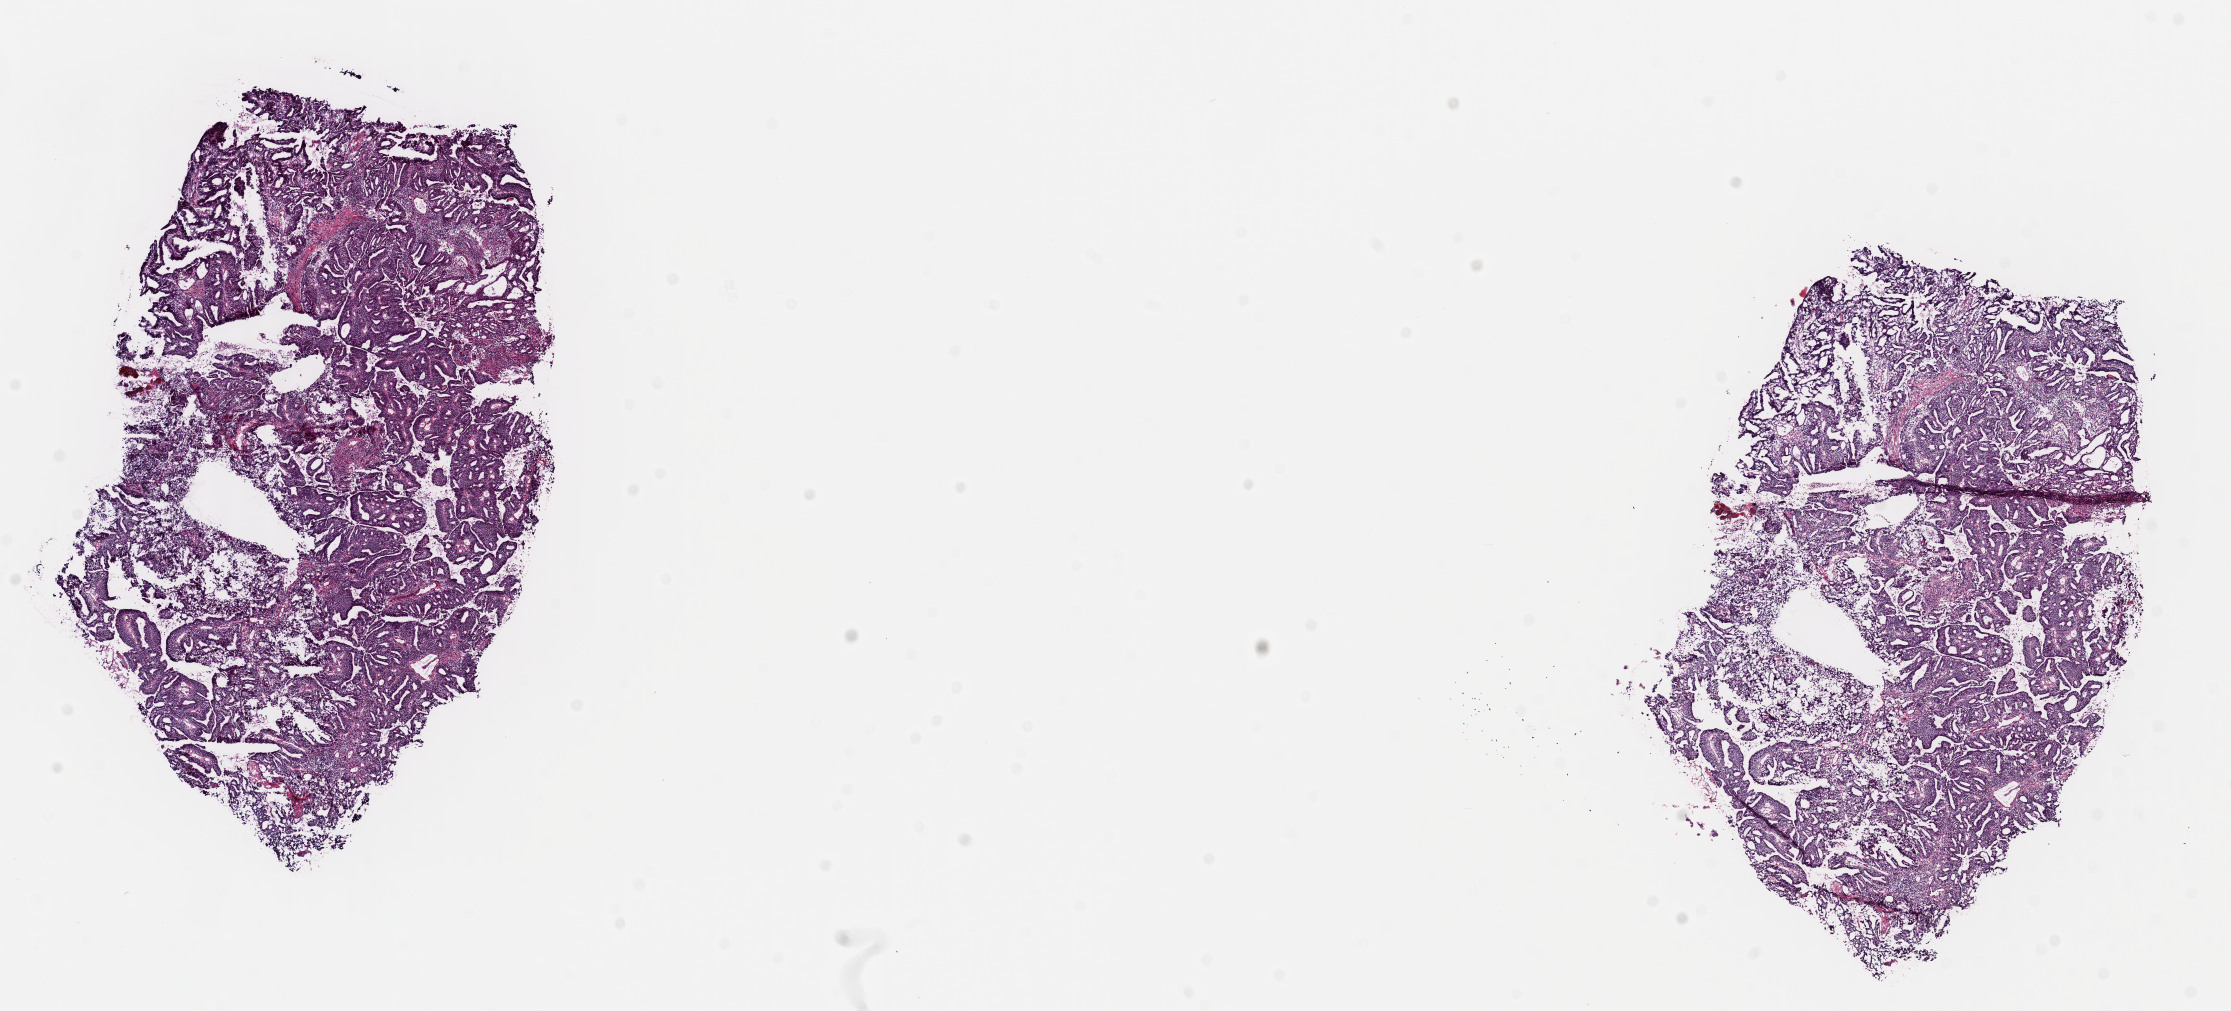
Whole-slide histology image, Hematoxylin and eosin (H&E) stained, whole scanned area (about 17.6 x 8.0 mm, from a 40x scan) shown as a low-resolution overview. Frozen section from the top of the tissue portion. Sample: primary tumour, cervix. Patient: female, age at initial diagnosis 56 years. Histologic grade: G2 (moderately differentiated). Pathologist review of this section (percent, as recorded): tumour cells 100%, tumour nuclei 75%, normal cells 0%, stromal cells 0%, necrosis 0%. Inflammatory infiltration, as recorded: lymphocyte infiltration 0%, monocyte infiltration 0%, neutrophil infiltration 0%.
• FIGO stage: IB2
• histologic diagnosis: Adenocarcinoma, NOS (cervix uteri)